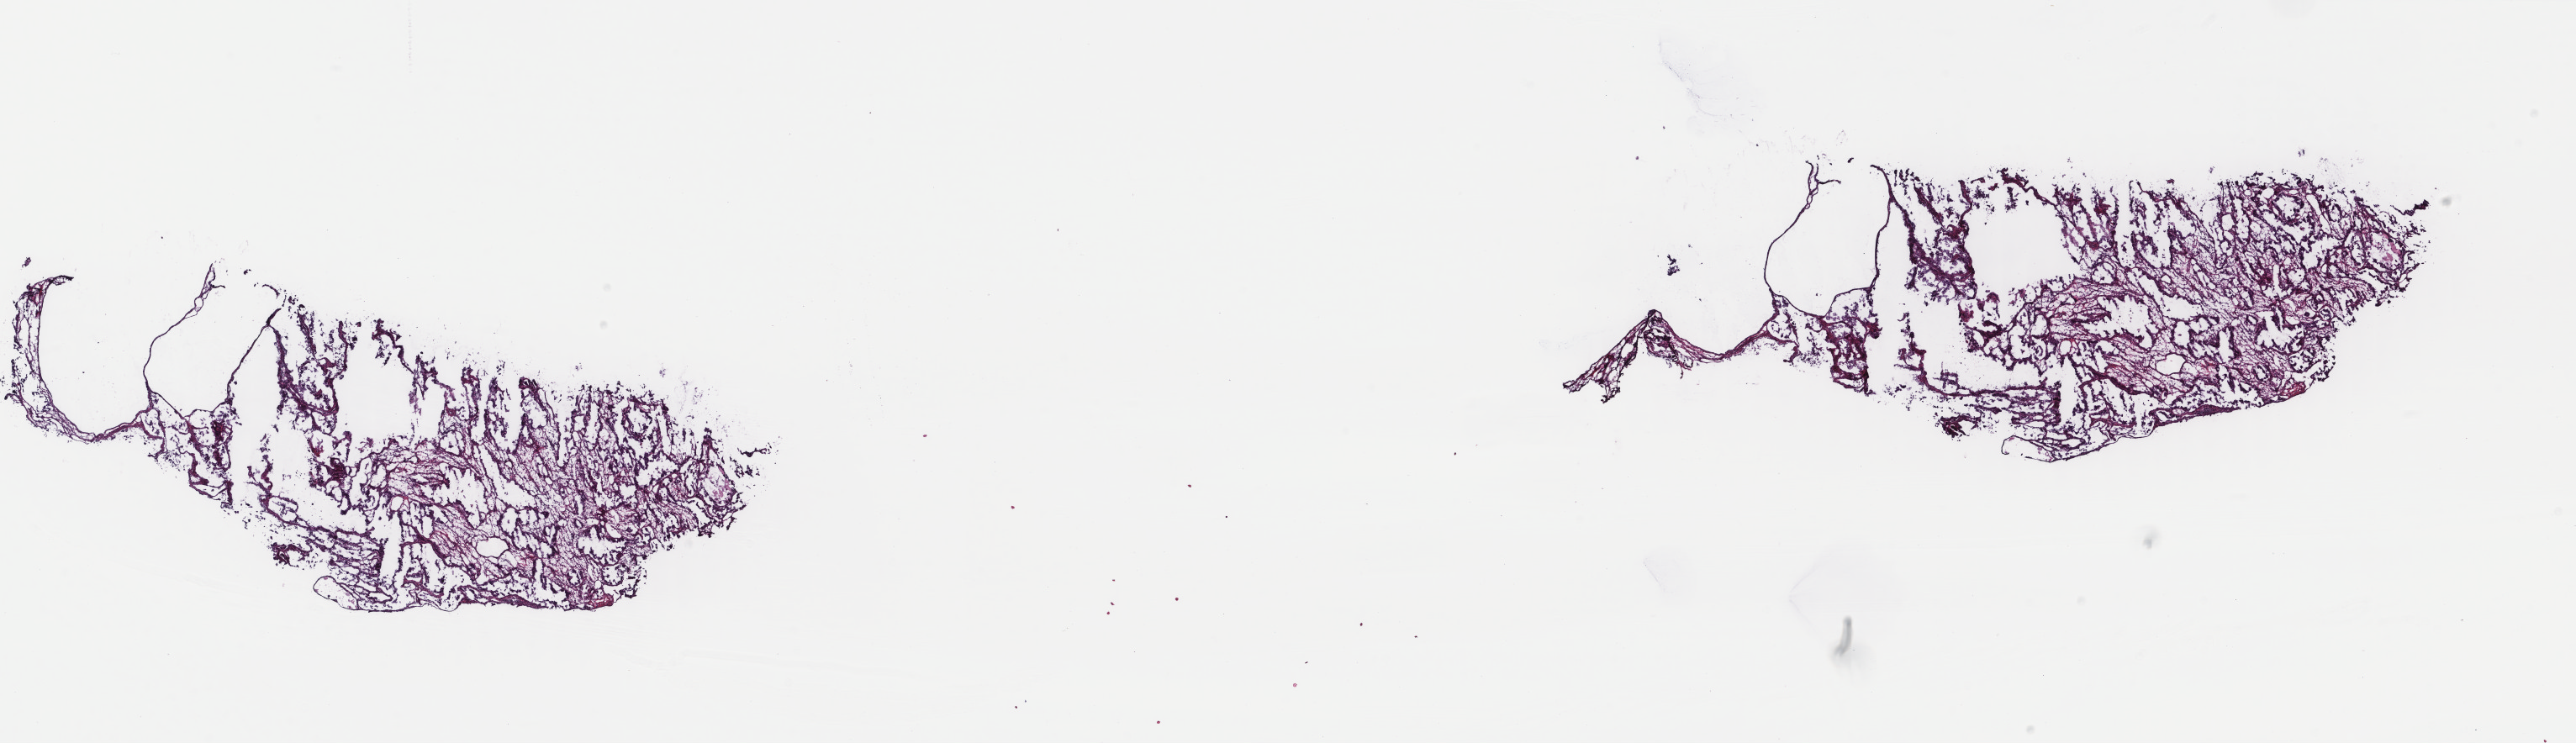
Whole-slide histology image, Hematoxylin and eosin (H&E) stained, low-resolution overview of the scanned area, about 24.3 x 7.0 mm; frozen section from the top of the tissue portion; primary tumour sample from the uterus. Female, age 76 years at initial diagnosis. Histologic grade: high grade. Pathologist review of this section (percent, as recorded): tumour cells 70%, tumour nuclei 70%, normal cells 0%, stromal cells 30%, necrosis 0%. Infiltration values recorded for this section: lymphocyte infiltration 3%, monocyte infiltration 4%, neutrophil infiltration 3%.
Lymph nodes positive (case pathology): 6 of 20 examined. FIGO stage: IIIC1. Pathologic diagnosis: Endometrioid adenocarcinoma, NOS (endometrium).